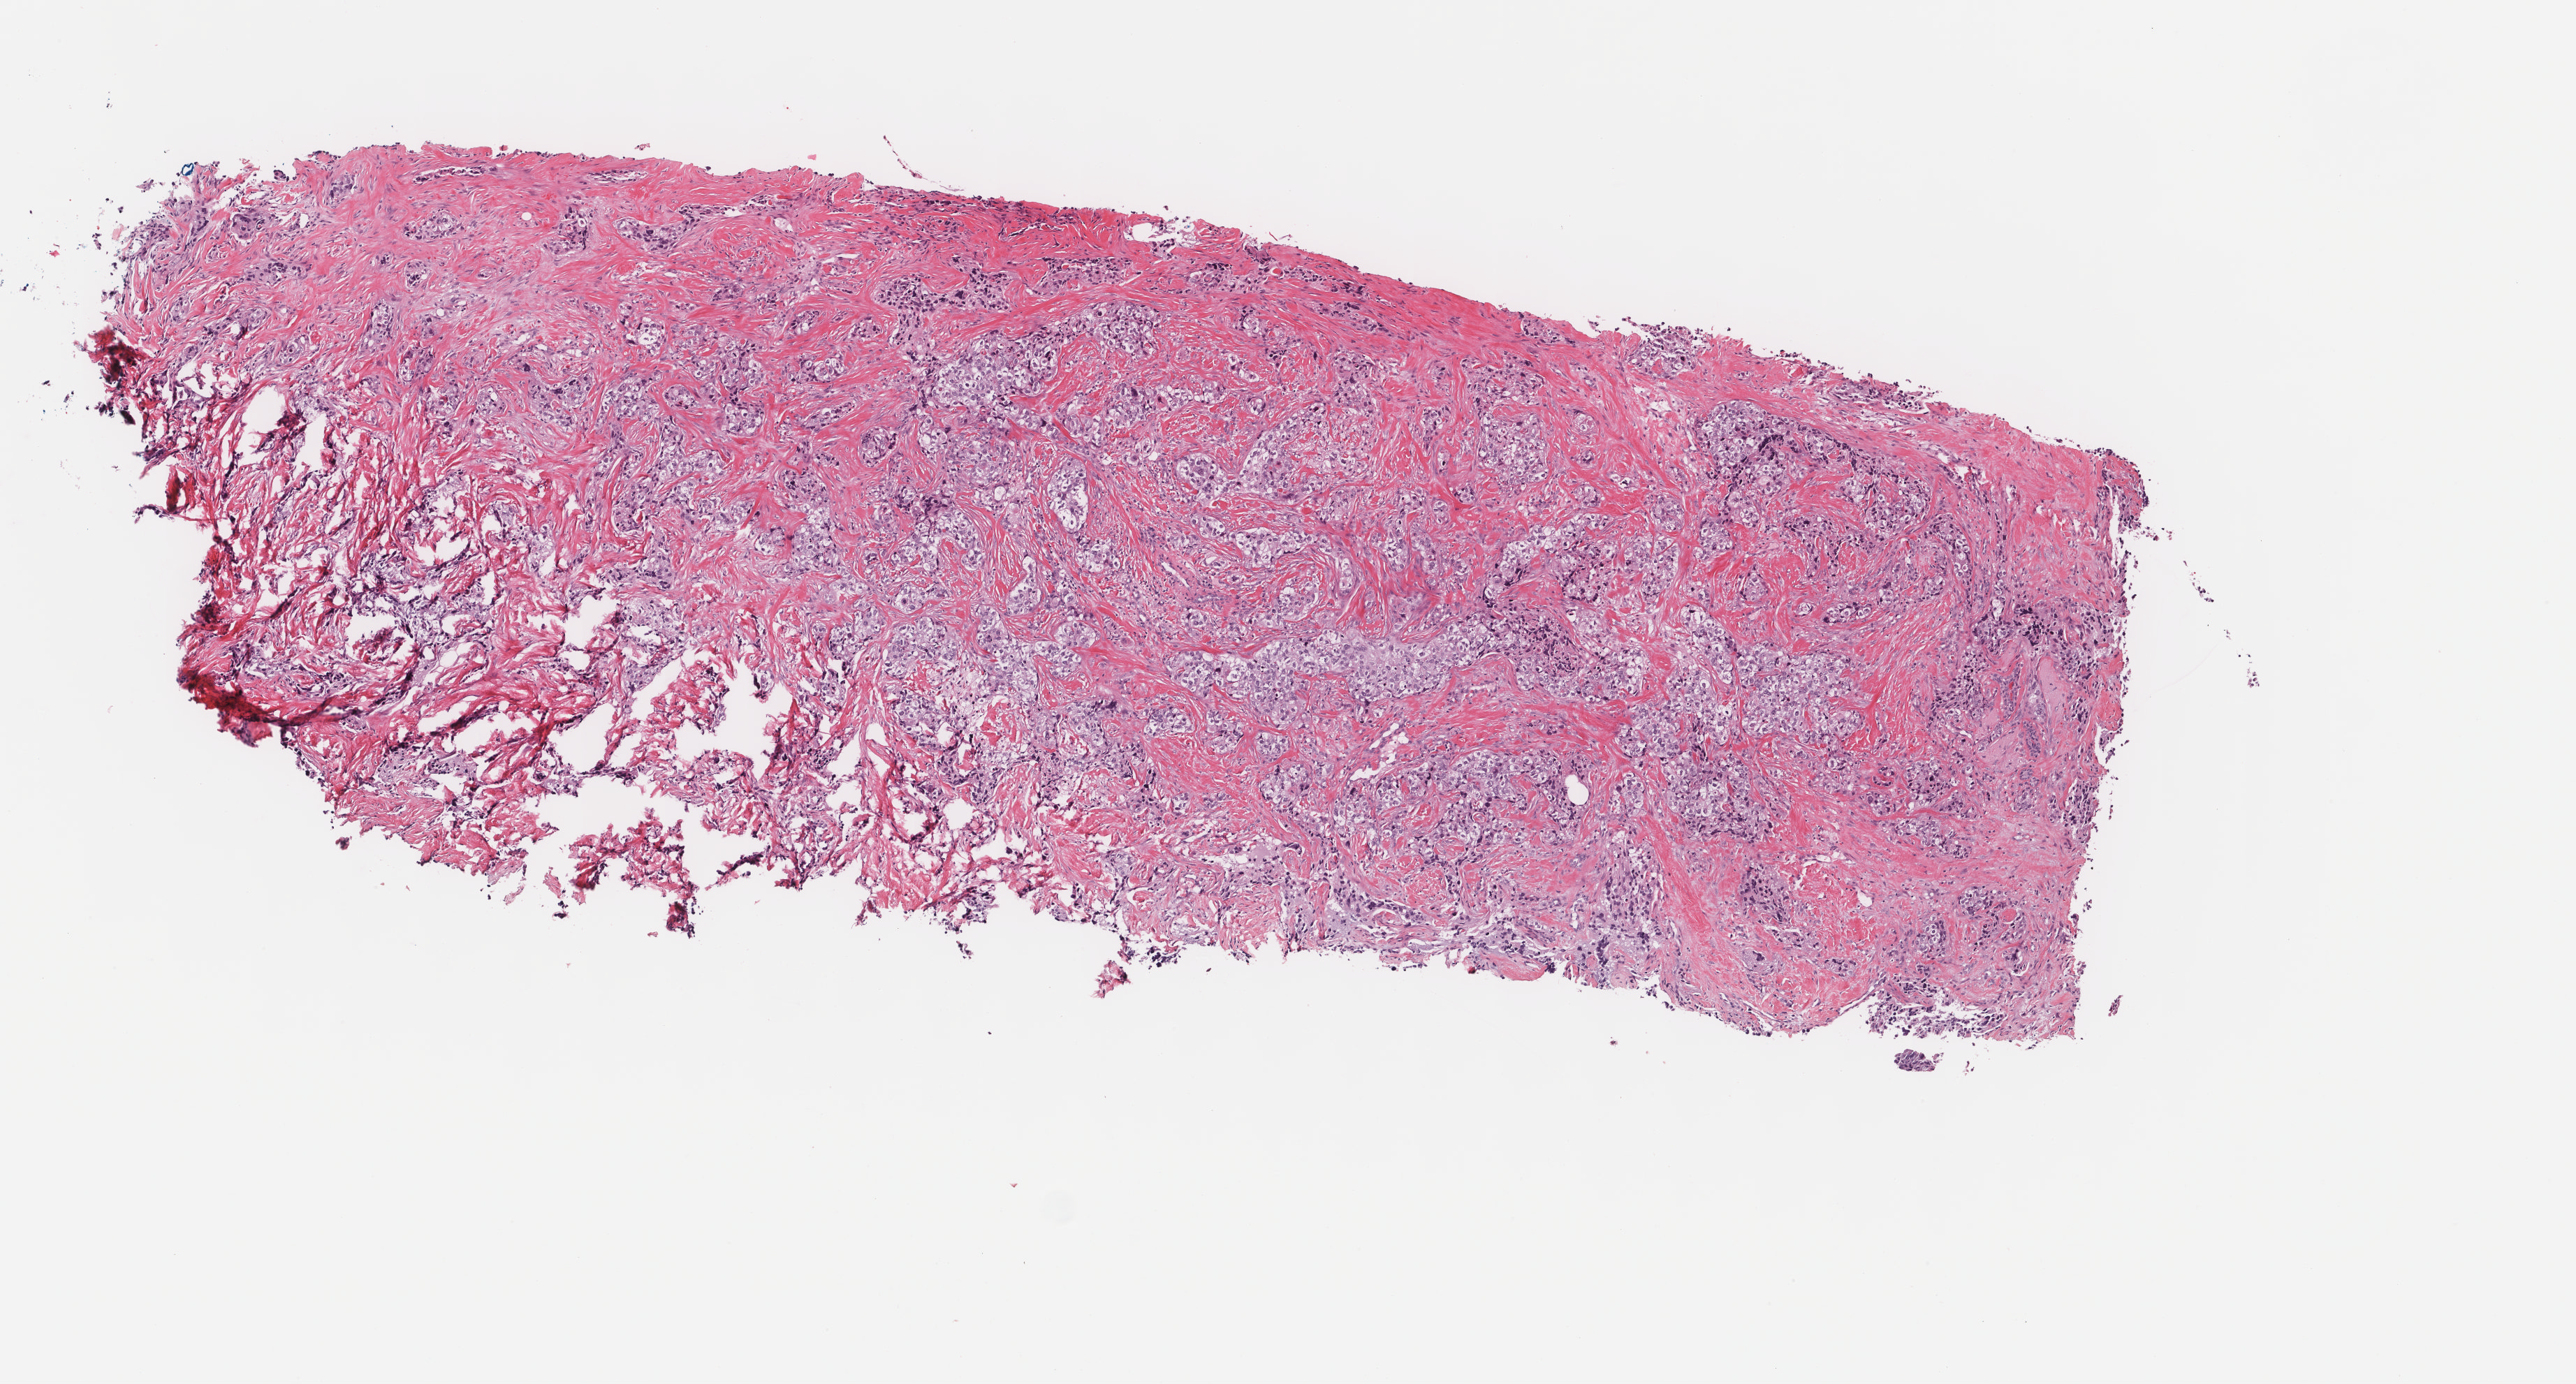
Whole-slide histology image, H&E-stained, shown as a low-resolution overview of the whole scanned area (about 7.3 x 3.9 mm). Frozen section. Sample: primary tumour, breast. Patient: female, age at initial diagnosis 65 years. Pathologist review of this section (percent, as recorded): tumour cells 50%, tumour nuclei 60%, normal cells 0%, stromal cells 50%, necrosis 0%. Inflammatory infiltration, as recorded: lymphocyte infiltration 0%, monocyte infiltration 0%, neutrophil infiltration 0%.
Lymph nodes positive (case pathology): 0 of 2 examined. AJCC pathologic stage: IIA (7th edition). Pathologic diagnosis: Infiltrating duct carcinoma, NOS.